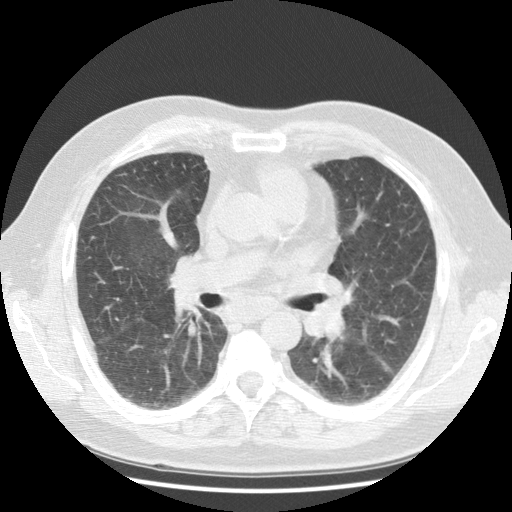
Low-dose screening chest CT, one axial slice; slice 64 of 108 in the series (ordered by position); 120 kVp; lung window (W 1500 / L -600 HU); 512 × 512 image matrix.
Outlined on this slice (outlined manually by an expert reader):
- lesion 1 (tumor, hilum of left lung): bounding box (x1, y1, x2, y2) in pixels: (302, 290, 353, 338)